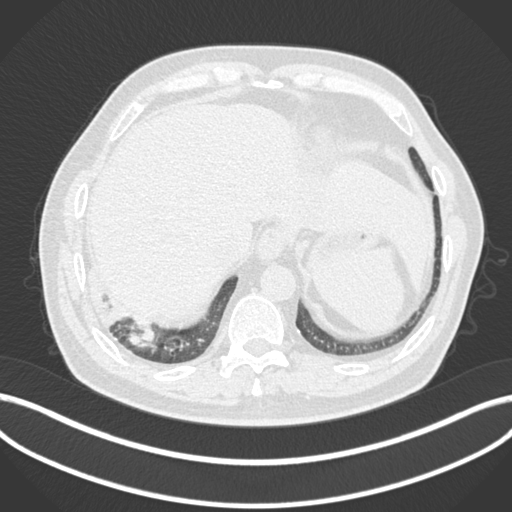
Chest CT, one axial slice. Position 16 of 200 along the scan axis. Reconstruction kernel B30f. Lung window (W 1500 / L -600 HU). 1 mm slice thickness. 512 × 512 image matrix, field of view 400 × 400 mm. Male patient, age 59 years.
Structures marked on this image (rectangle marked by the reading radiologist):
- lung tumour (recorded histology: adenocarcinoma): bounding box (x1, y1, x2, y2) in pixels: (126, 318, 157, 353)